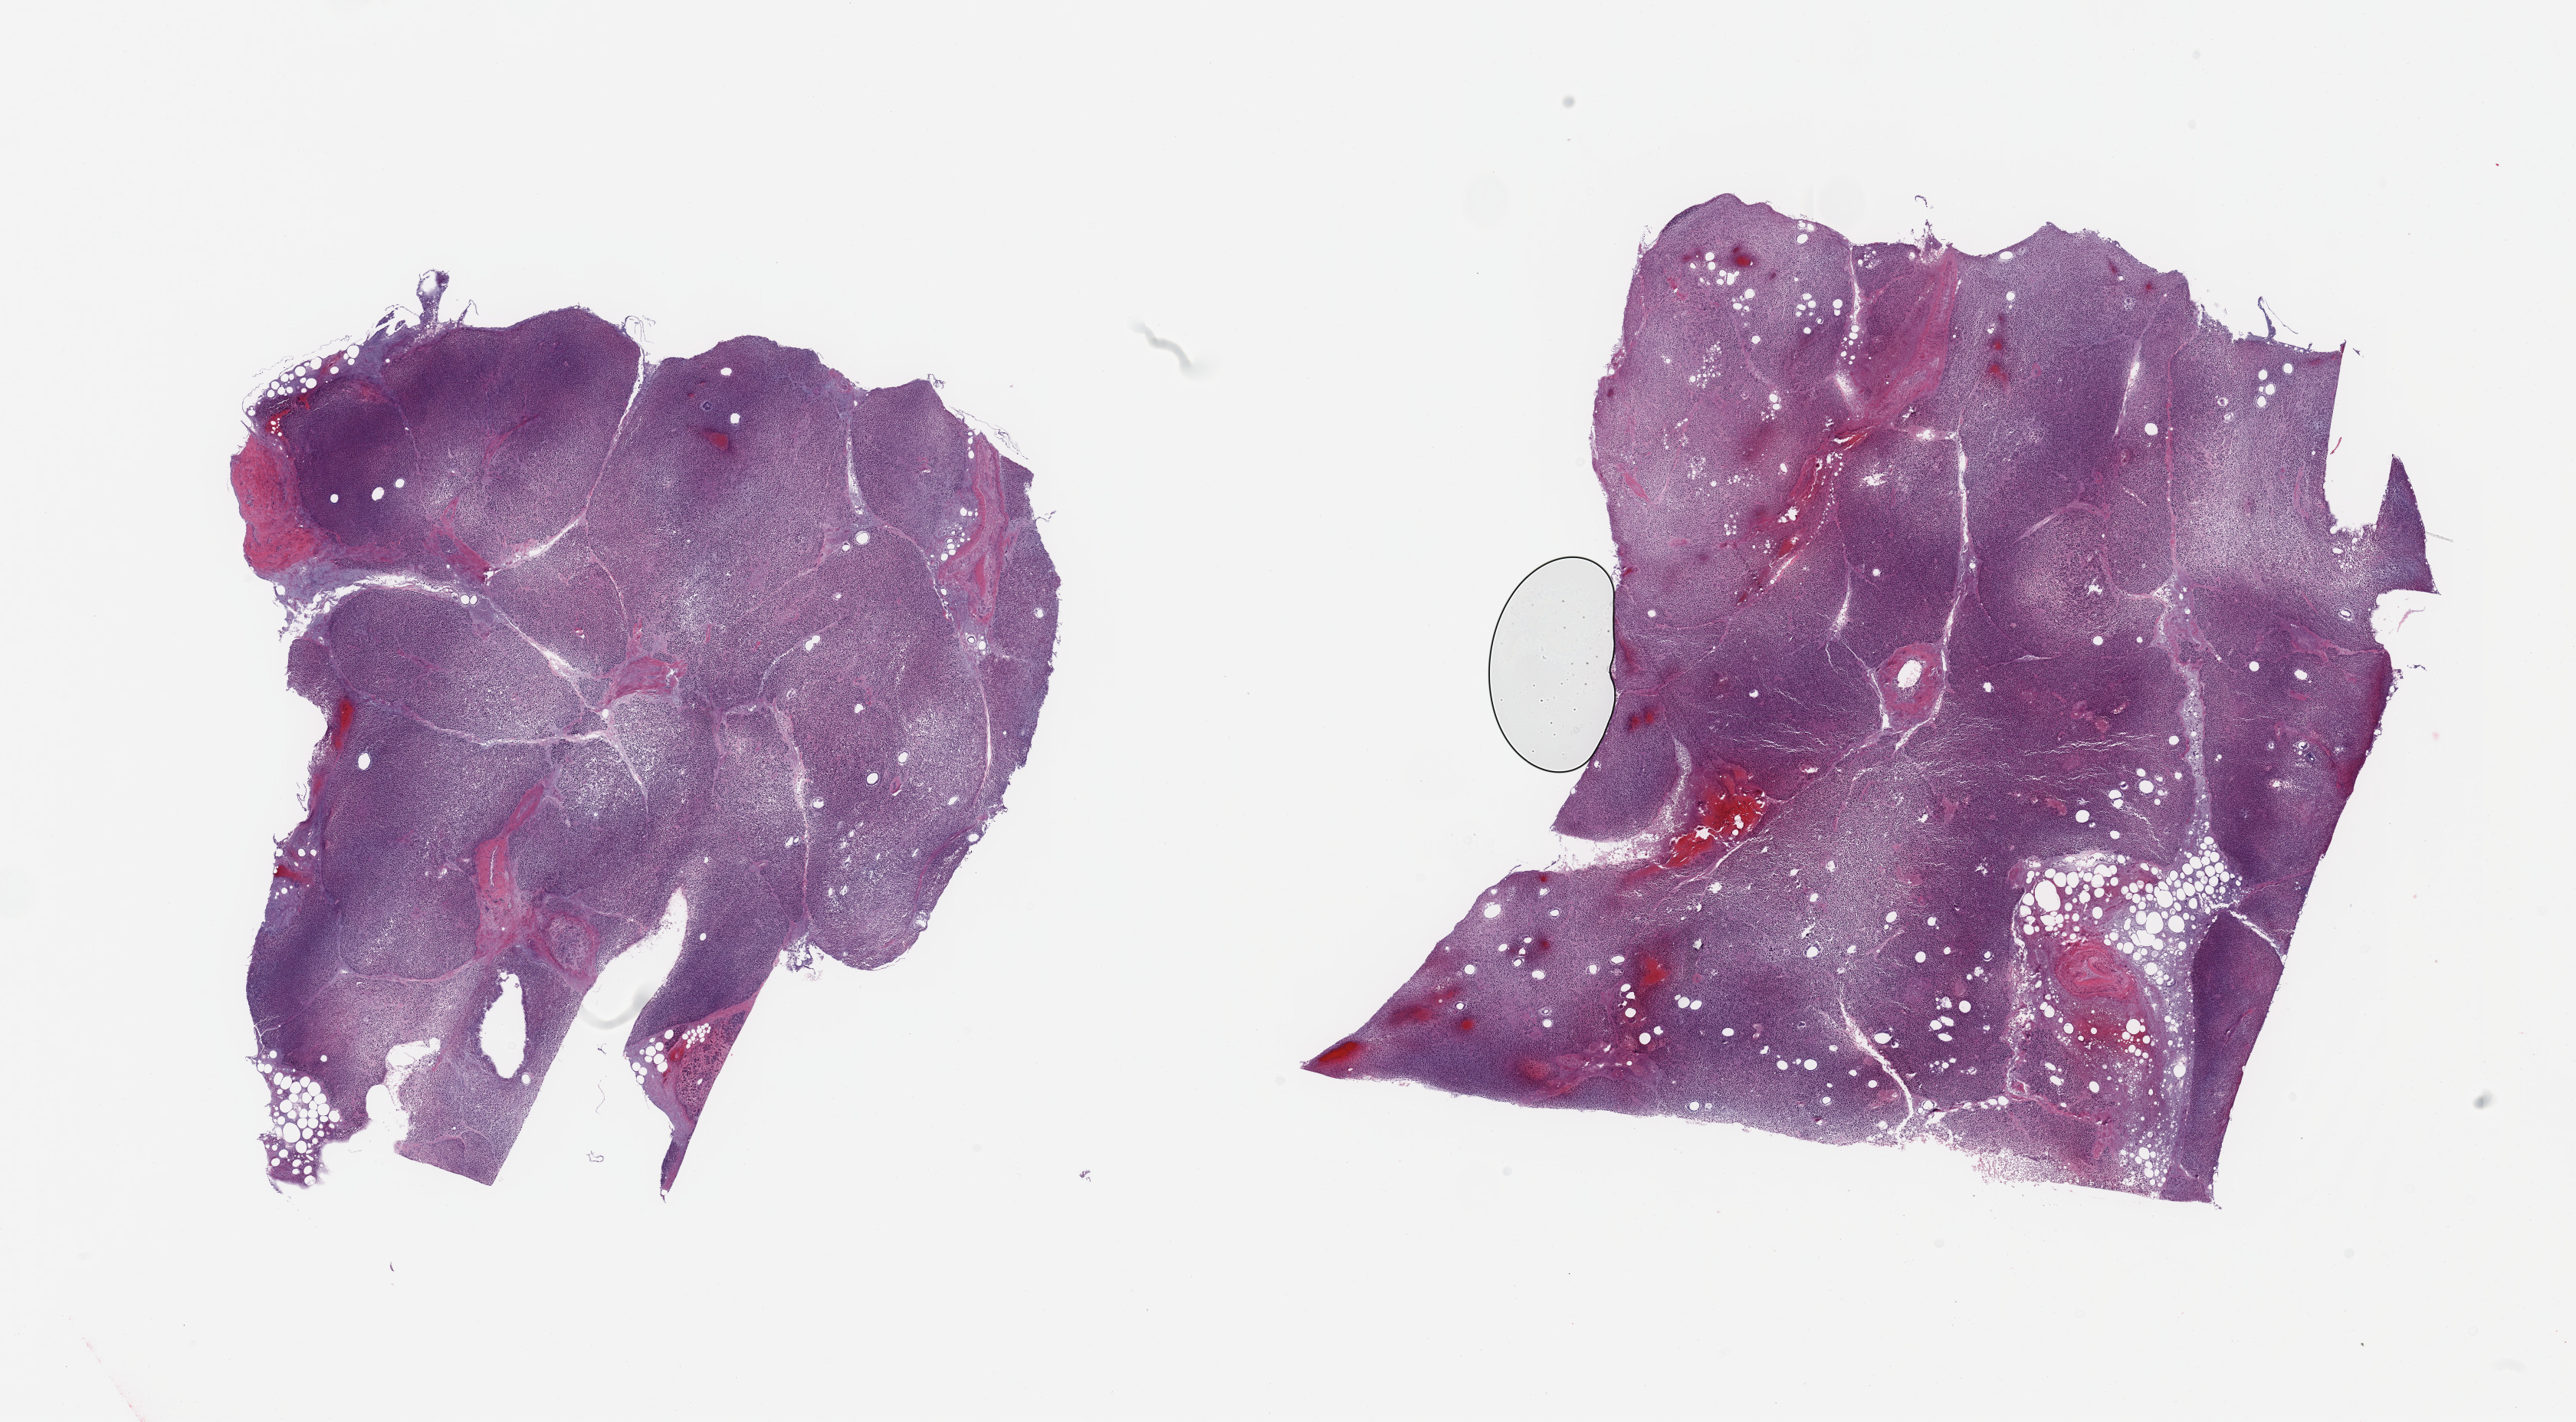
Whole-slide image, haematoxylin and eosin stain, brightfield, whole scanned area (about 26.6 x 14.7 mm, from a 20x scan) shown as a low-resolution overview. PAXgene-fixed paraffin-embedded (PFPE) section. Target tissue: pancreas. Donor tissue sample. Male donor.
Reviewer comment on this tissue sample: 2 pieces; severely autolyzed pancreas.